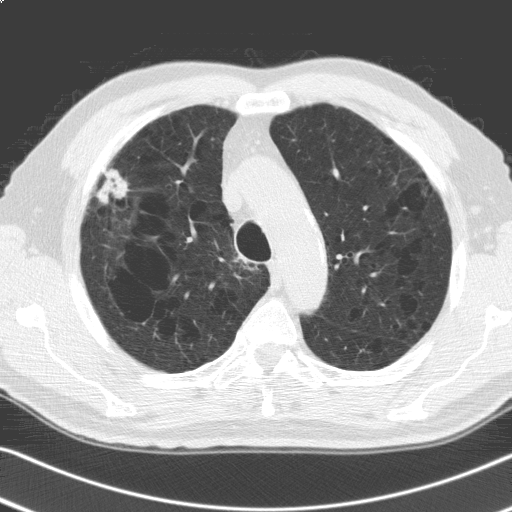
Chest CT (low-dose screening protocol), one axial image. Second screening round (one year after baseline). Lung window (W 1500 / L -600 HU). Slice 39 of 168 in the series. 512 × 512 image matrix. Male, age 69 years at enrolment. Former smoker at enrolment.
Lesion marked by an expert reader, bounding box <87,166,132,216> (left, top, right, bottom; pixels). The screening reader recorded 6 non-calcified nodules or masses ≥4 mm on this exam (right upper lobe, right upper lobe, right lower lobe, lingula, left lower lobe, left lower lobe); which of them this box marks is not recorded. Later outcome: lung cancer diagnosed 91 days after this screen — adenosquamous carcinoma, right upper lobe, poorly differentiated (G3), stage IV (AJCC 6th edition), 30 mm at pathology.